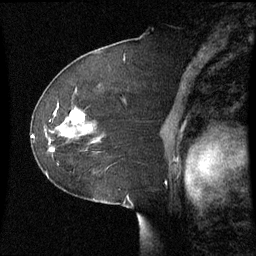
Breast MRI (dynamic contrast-enhanced), one sagittal slice; slice 40 of 60 in the series (ordered by position); dynamic contrast-enhanced series, image 2 of 3 at this slice position (ordered by acquisition); 1.5 T; TE 4.2 ms, TR 8.9 ms; 256 × 256 image matrix, field of view 220 × 220 mm. Female patient, age 51 years. Case-level facts recorded for this patient, not image findings: setting: breast cancer imaged before/during neoadjuvant chemotherapy; receptor status: HR-positive, HER2-negative.
Annotated regions visible in this slice (semi-automatic segmentation, software-assisted and operator-edited):
- analysis volume of interest (the breast-tissue region the enhancement analysis was run in; not a lesion): box from (x=44, y=106) to (x=101, y=165) px
- tumour enhancement mask (voxels above the 70 % enhancement threshold inside the analysis volume of interest): (x=70, y=110)–(x=85, y=123)